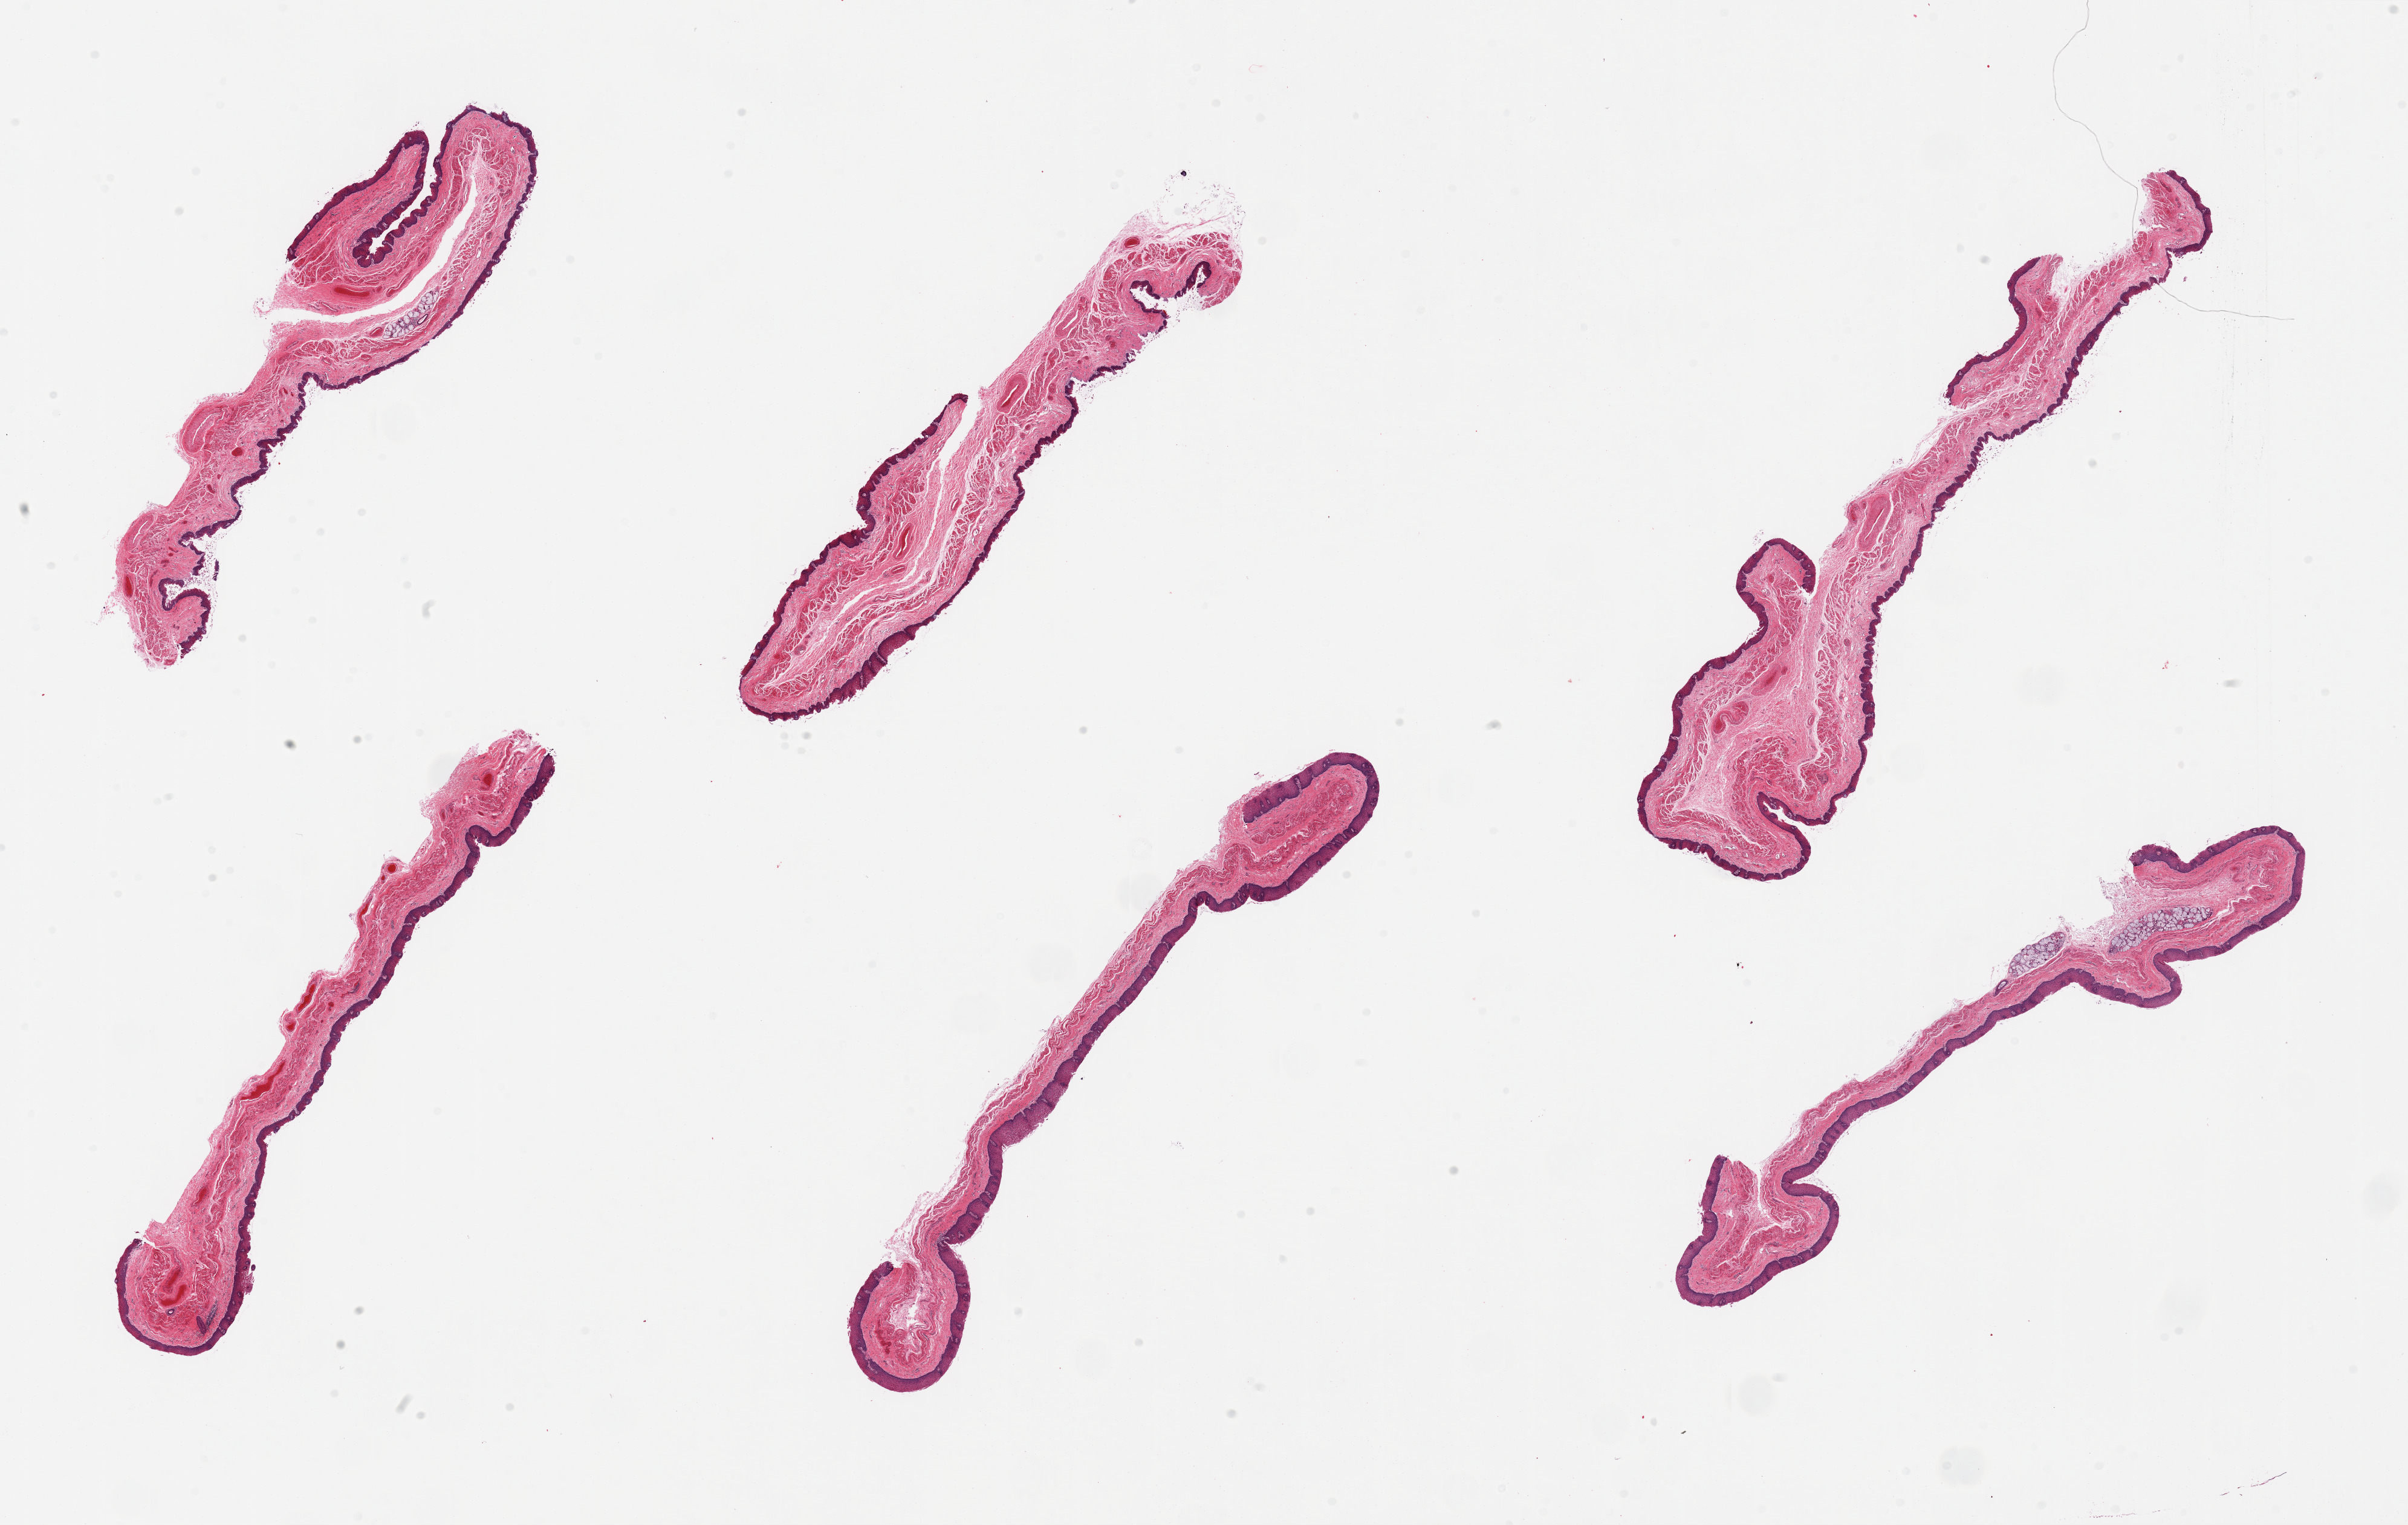
H&E whole-slide image, a low-resolution overview of the entire scanned area, about 31.5 x 20.0 mm. PAXgene-fixed, paraffin-embedded tissue. Sampled site (target tissue): esophageal mucous membrane. Donor tissue sample. Male donor.
Review note (as recorded): 6 pieces, squamous mucosa is ~5% thickness.